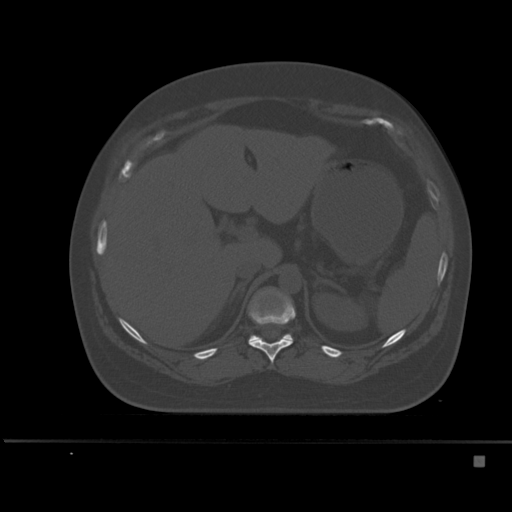
CT including the spine, one axial slice; slice 226 of 495 in the series (ordered by position); bone window (W 1800 / L 400 HU); 1.5 mm slice thickness; 512 × 512 image matrix. Patient: female, 33 years. Case-level facts recorded for this patient, not image findings: primary cancer: breast; vertebrae with lytic lesions (as recorded): T1.
Outlined on this slice (semi-automatic segmentation, software-assisted and operator-edited):
- T11 vertebra: bounding box <249,289,296,363> (left, top, right, bottom; pixels)
- T12 vertebra: <248,334,292,343>